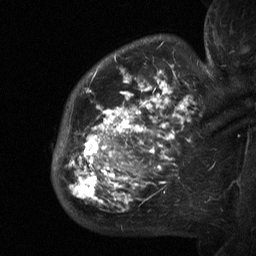
Breast MRI (dynamic contrast-enhanced), one sagittal slice. Slice 47 of 64 in the series (ordered by position). Dynamic contrast-enhanced study with each time point stored as its own series, time point 2 of 3 at this slice position (early post-contrast, ordered by acquisition time). 1.5 T. TE 4.8 ms, TR 27 ms. 2.3 mm slice thickness. 256 × 256 image matrix, field of view 200 × 200 mm. Female patient, age 50 years. From the clinical record (not read from this slice): setting: breast cancer imaged before/during neoadjuvant chemotherapy; receptor status: HER2-positive.
Annotated regions visible in this slice (semi-automatic segmentation, software-assisted and operator-edited):
- analysis volume of interest (the breast-tissue region the enhancement analysis was run in; not a lesion): bounding box <53,64,211,218> (left, top, right, bottom; pixels)
- tumour enhancement mask (voxels above the 90 % enhancement threshold inside the analysis volume of interest): <68,68,195,212>